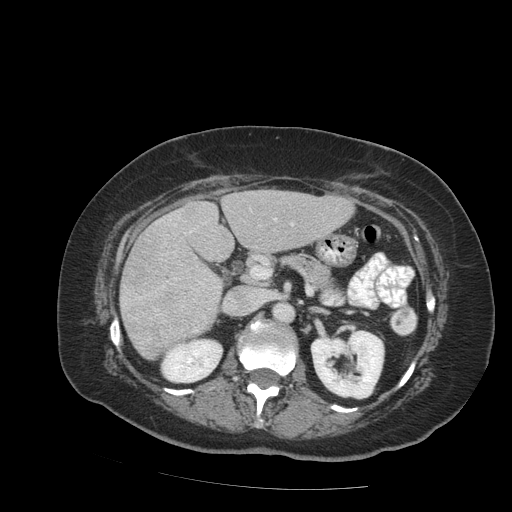
Contrast-enhanced abdominal CT (liver protocol), one axial slice. Slice 41 of 99 in the series (ordered by position). Reconstruction kernel STANDARD. 140 kVp. Soft-tissue window (W 400 / L 40 HU). 2.5 mm slice thickness. 512 × 512 image matrix. Case-level facts recorded for this patient, not image findings: diagnosis: hepatocellular carcinoma (patient treated with transarterial chemoembolisation; whether this scan precedes or follows treatment is not stated here); TNM stage (as recorded): Stage-IVB; Child-Pugh class: A; tumour differentiation: moderately differentiated.
Annotated regions visible in this slice (semi-automatic segmentation, software-assisted and operator-edited):
- liver parenchyma outside the tumour (the mass and vessels are separate outlines, so this box may not span the whole liver): box from (x=120, y=190) to (x=354, y=358) px
- mass: (x=122, y=237)–(x=218, y=356)
- liver vessels: (x=160, y=218)–(x=293, y=233)